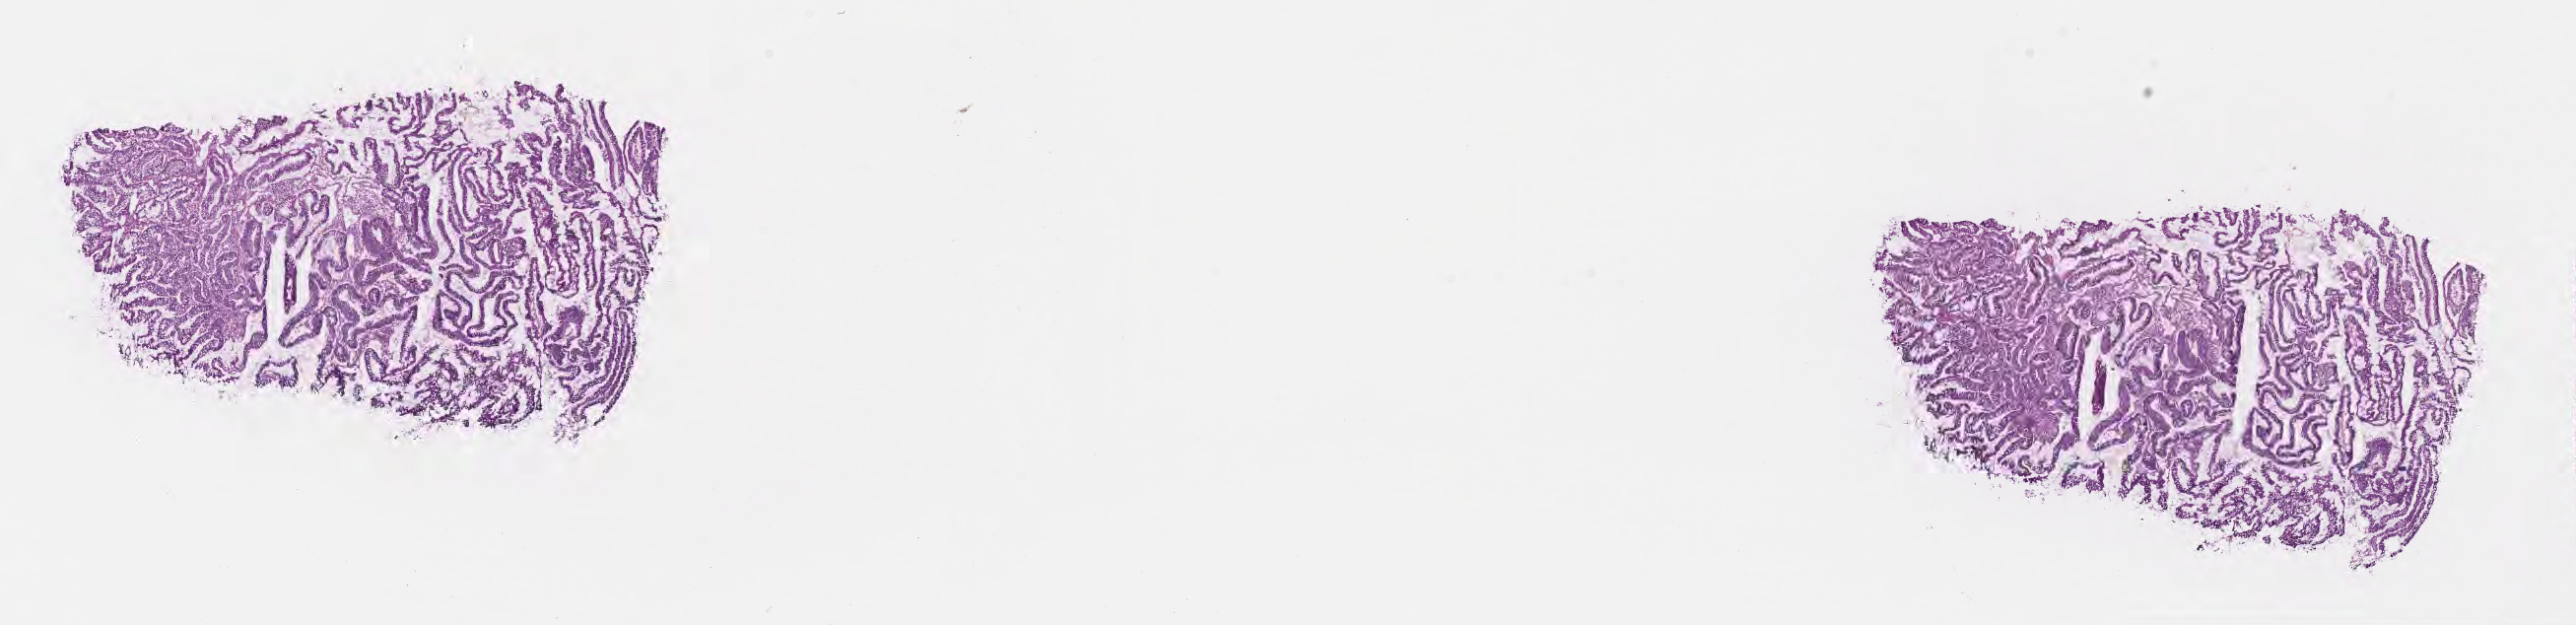
Digitized H&E-stained section, whole scanned area (about 21.1 x 5.1 mm) shown as a low-resolution overview, frozen section, premalignant lesion from a patient with tubulovillous adenoma, NOS, site: cecum. Female, age 62 years at initial diagnosis. Pathologist review of this section (percent, as recorded): tumor cells 84%, tumor nuclei 83%, stromal cells 16%, necrosis 0%, normal cells 0%. Inflammatory infiltration, as recorded: lymphocyte infiltration 14%, monocyte infiltration 1%, neutrophil infiltration 0%.
• this section: sample classed premalignant; the patient's recorded diagnosis is given above
• section: top of the tissue portion